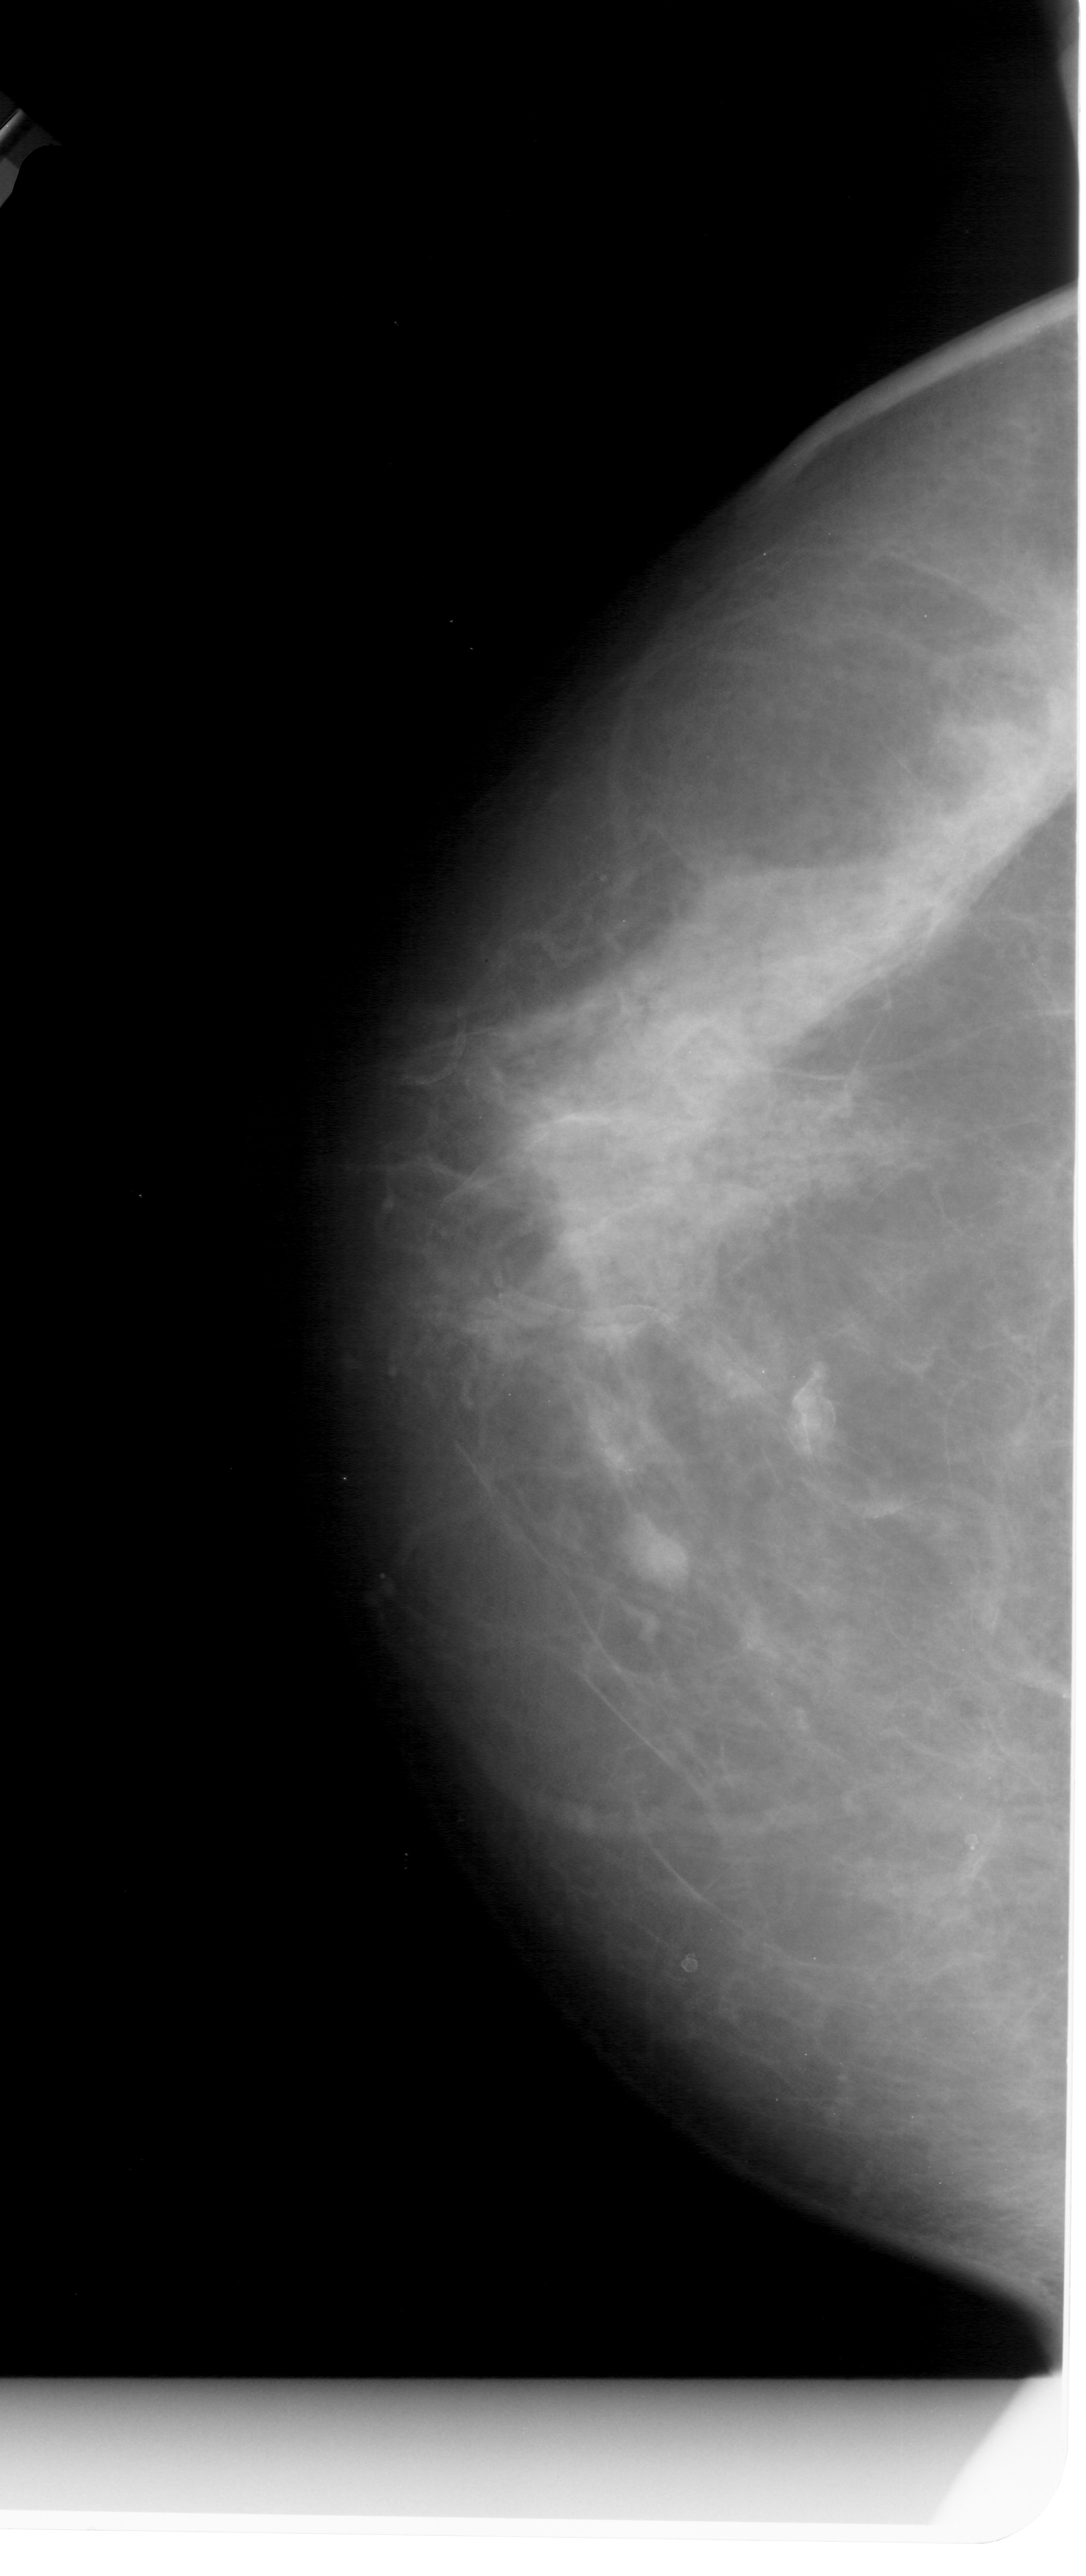
Digitized screen-film mammogram. Left breast. CC view. BI-RADS breast density category 4 (scale 1–4). 1086 × 2576 image matrix.
Marked abnormalities (boxes around the expert regions of interest):
- mass, shape irregular, margins ill defined; BI-RADS assessment category 4; pathology result (as recorded, not read from the image): benign: box from (x=612, y=1501) to (x=701, y=1594) px